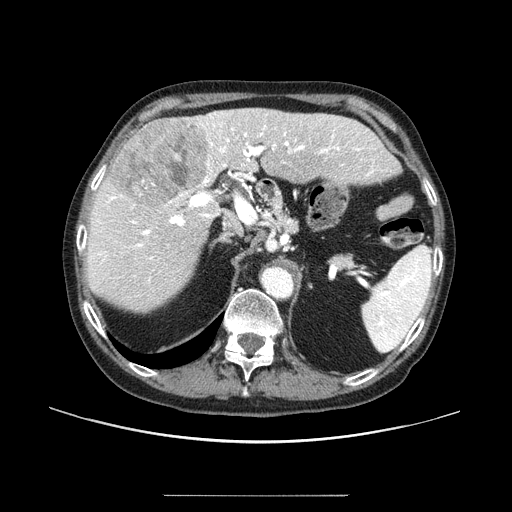
Contrast-enhanced abdominal CT (liver protocol), one axial slice. One of 2 acquisitions stored at this slice position. Soft-tissue window (W 400 / L 40 HU). 2.5 mm slice thickness. 512 × 512 image matrix, field of view 400 × 400 mm. From the clinical record (not read from this slice): diagnosis: hepatocellular carcinoma (patient treated with transarterial chemoembolisation; whether this scan precedes or follows treatment is not stated here); TNM stage (as recorded): Stage-I; Child-Pugh class: A.
Structures marked on this image (semi-automatically segmented with operator editing):
- liver parenchyma outside the tumour (the mass and vessels are separate outlines, so this box may not span the whole liver): bounding box <86,108,396,310> (left, top, right, bottom; pixels)
- mass: <110,117,211,212>
- liver vessels: <90,112,375,282>